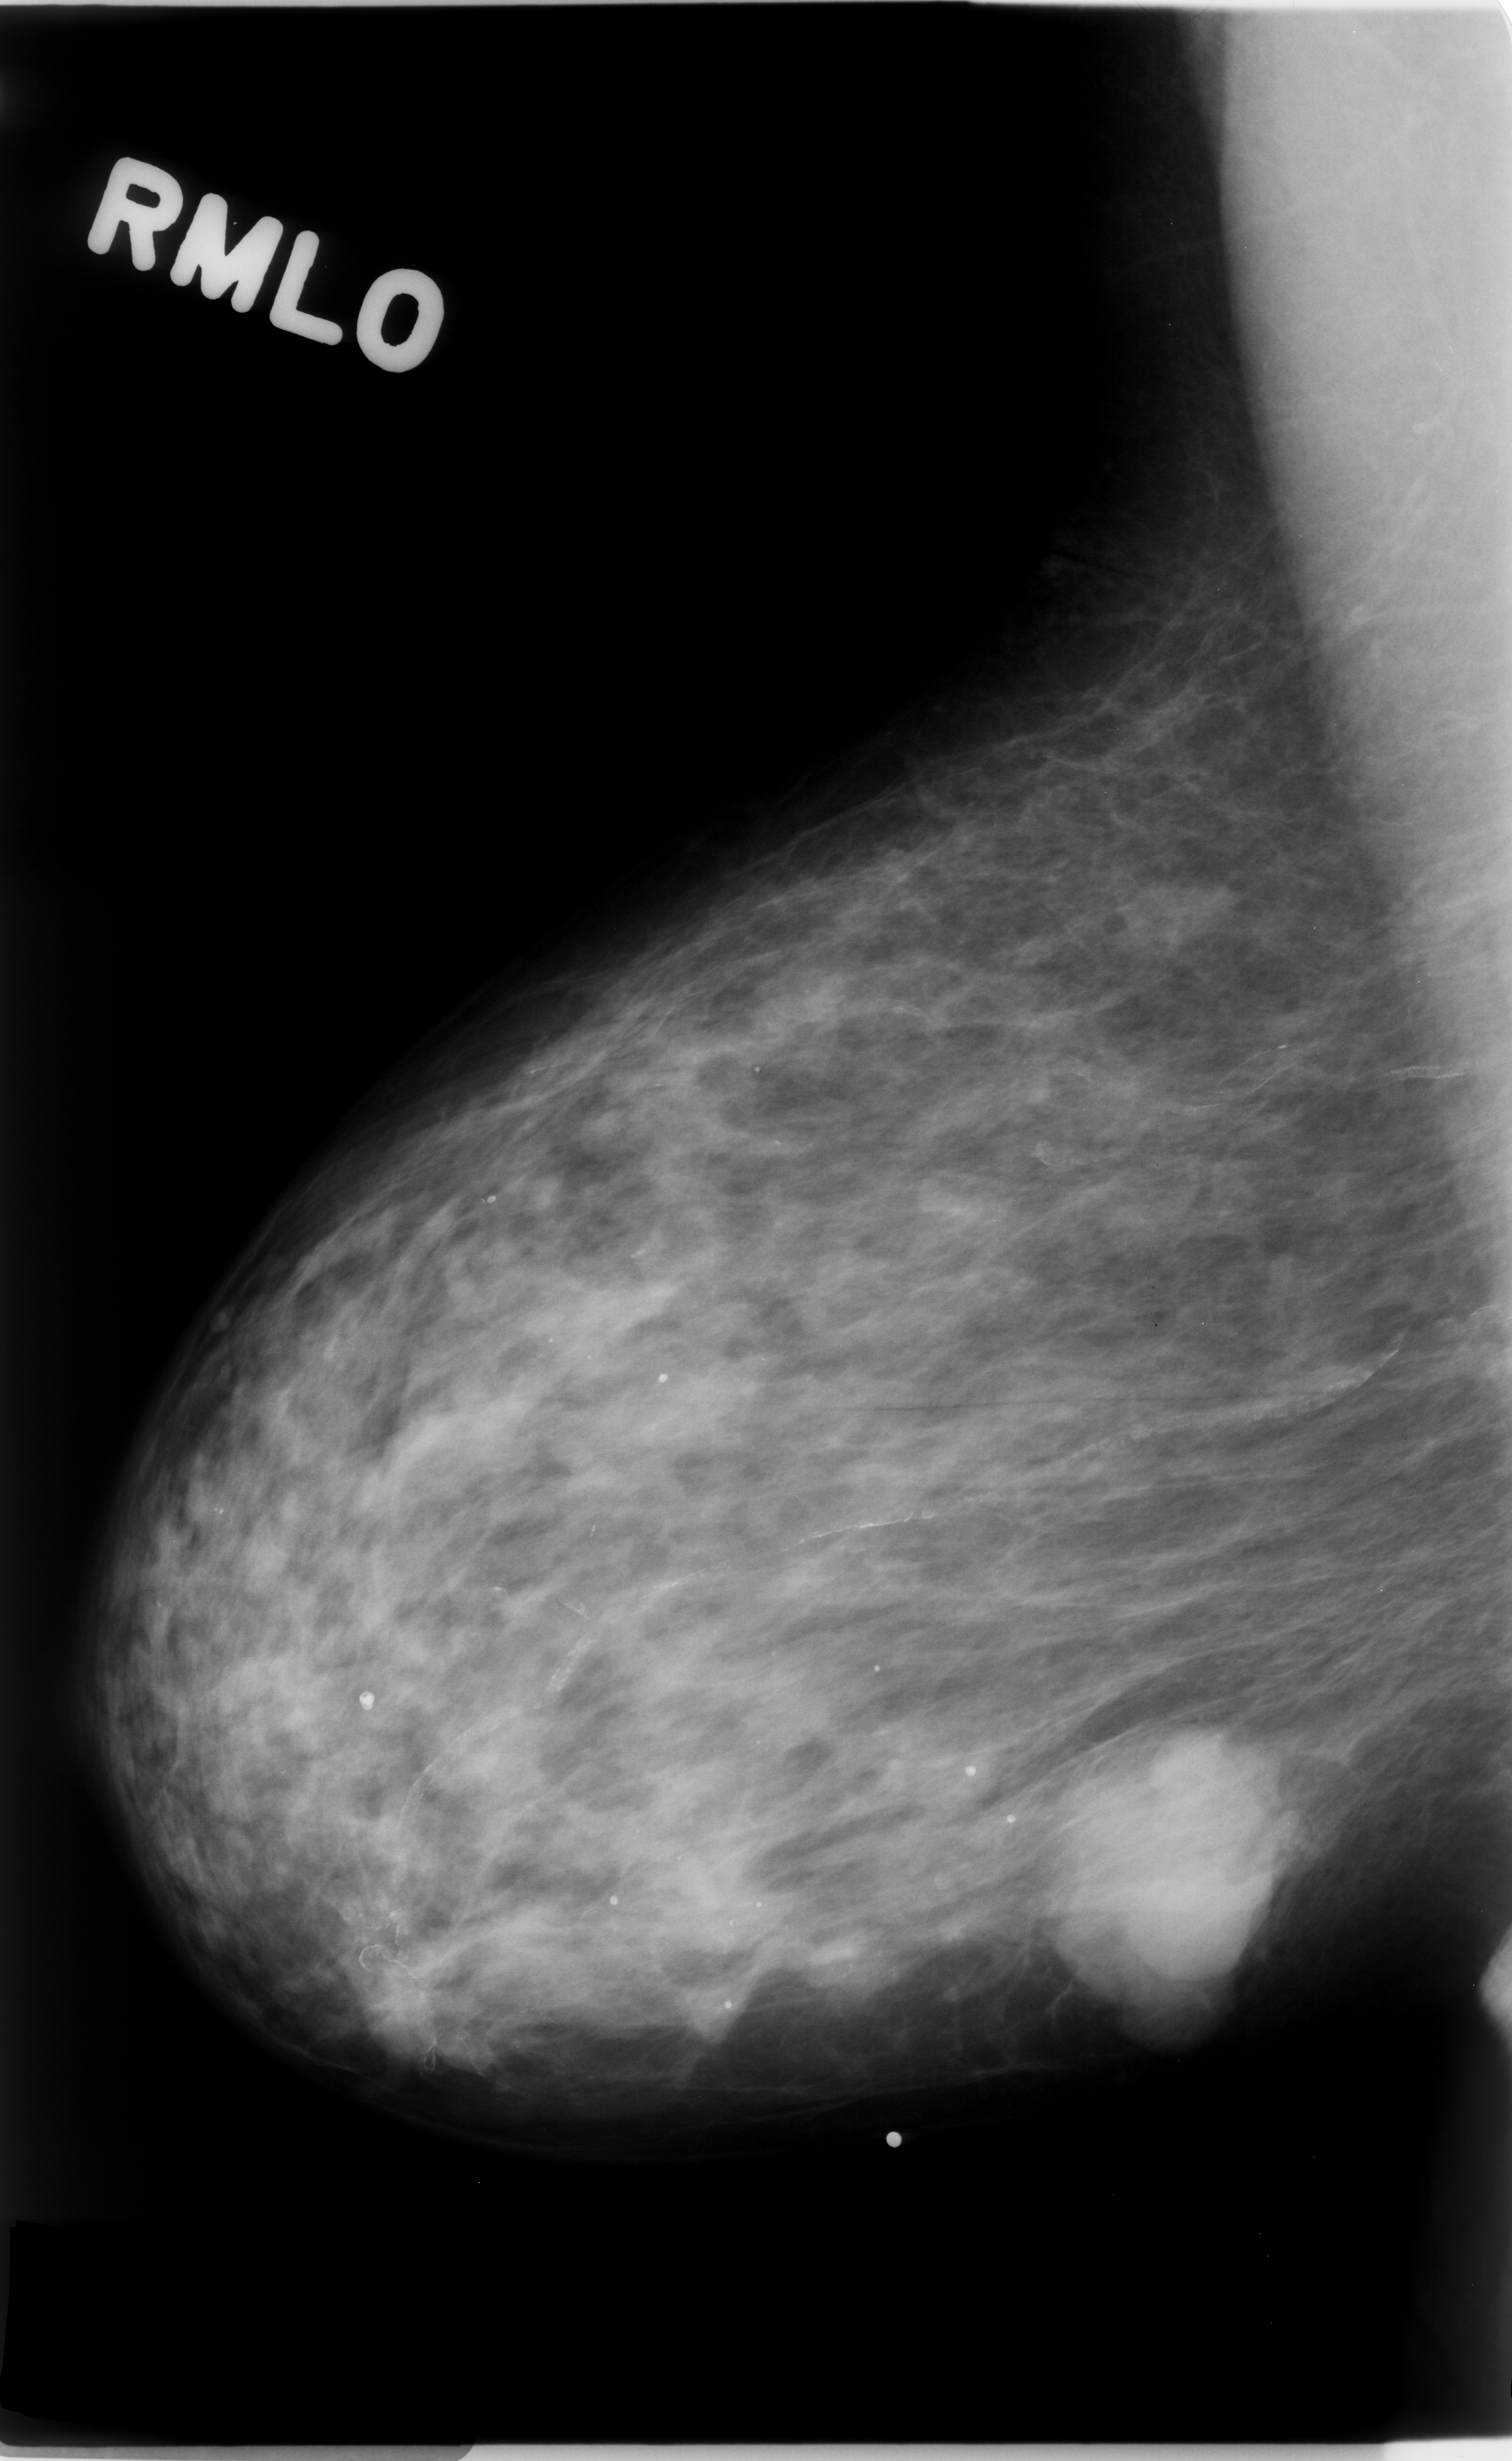
Digitized screen-film mammogram, right breast, MLO view, BI-RADS breast density category 2 (scale 1–4).
Radiologist-marked abnormalities on this image: mass, shape lobulated, margins microlobulated; BI-RADS assessment category 5; pathology result (as recorded, not read from the image): malignant.